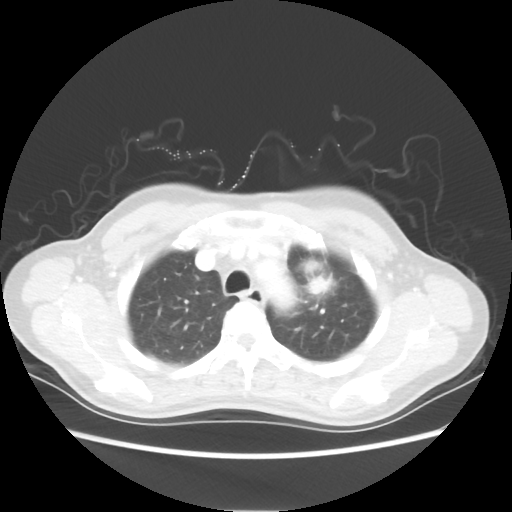
Chest CT, one axial slice; position 43 of 54 along the scan axis; reconstruction kernel STANDARD; 80 kVp; lung window (W 1500 / L -600 HU); 5 mm slice thickness; 512 × 512 image matrix. Patient: female, 53 years. Case-level facts recorded for this patient, not image findings: clinical TNM (as recorded): T1c N0 M0.
Structures marked on this image (rectangle marked by the reading radiologist):
- lung tumour (recorded histology: adenocarcinoma): bounding box (x1, y1, x2, y2) in pixels: (297, 256, 345, 303)
- lung tumour (recorded histology: adenocarcinoma): (303, 256, 328, 300)